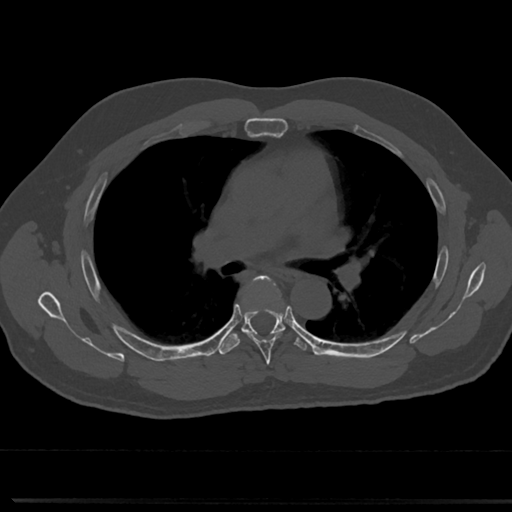
CT including the spine, one axial slice; slice 477 of 817 in the series (ordered by position); reconstruction kernel Br40s/3; 120 kVp; bone window (W 1800 / L 400 HU); 0.5 mm slice thickness; 512 × 512 image matrix, field of view 355 × 355 mm. Male patient, age 61 years. From the clinical record (not read from this slice): primary cancer: prostate.
Structures marked on this image (semi-automatic segmentation, software-assisted and operator-edited):
- T5 vertebra: box from (x=238, y=277) to (x=288, y=360) px
- T6 vertebra: (x=224, y=323)–(x=287, y=348)